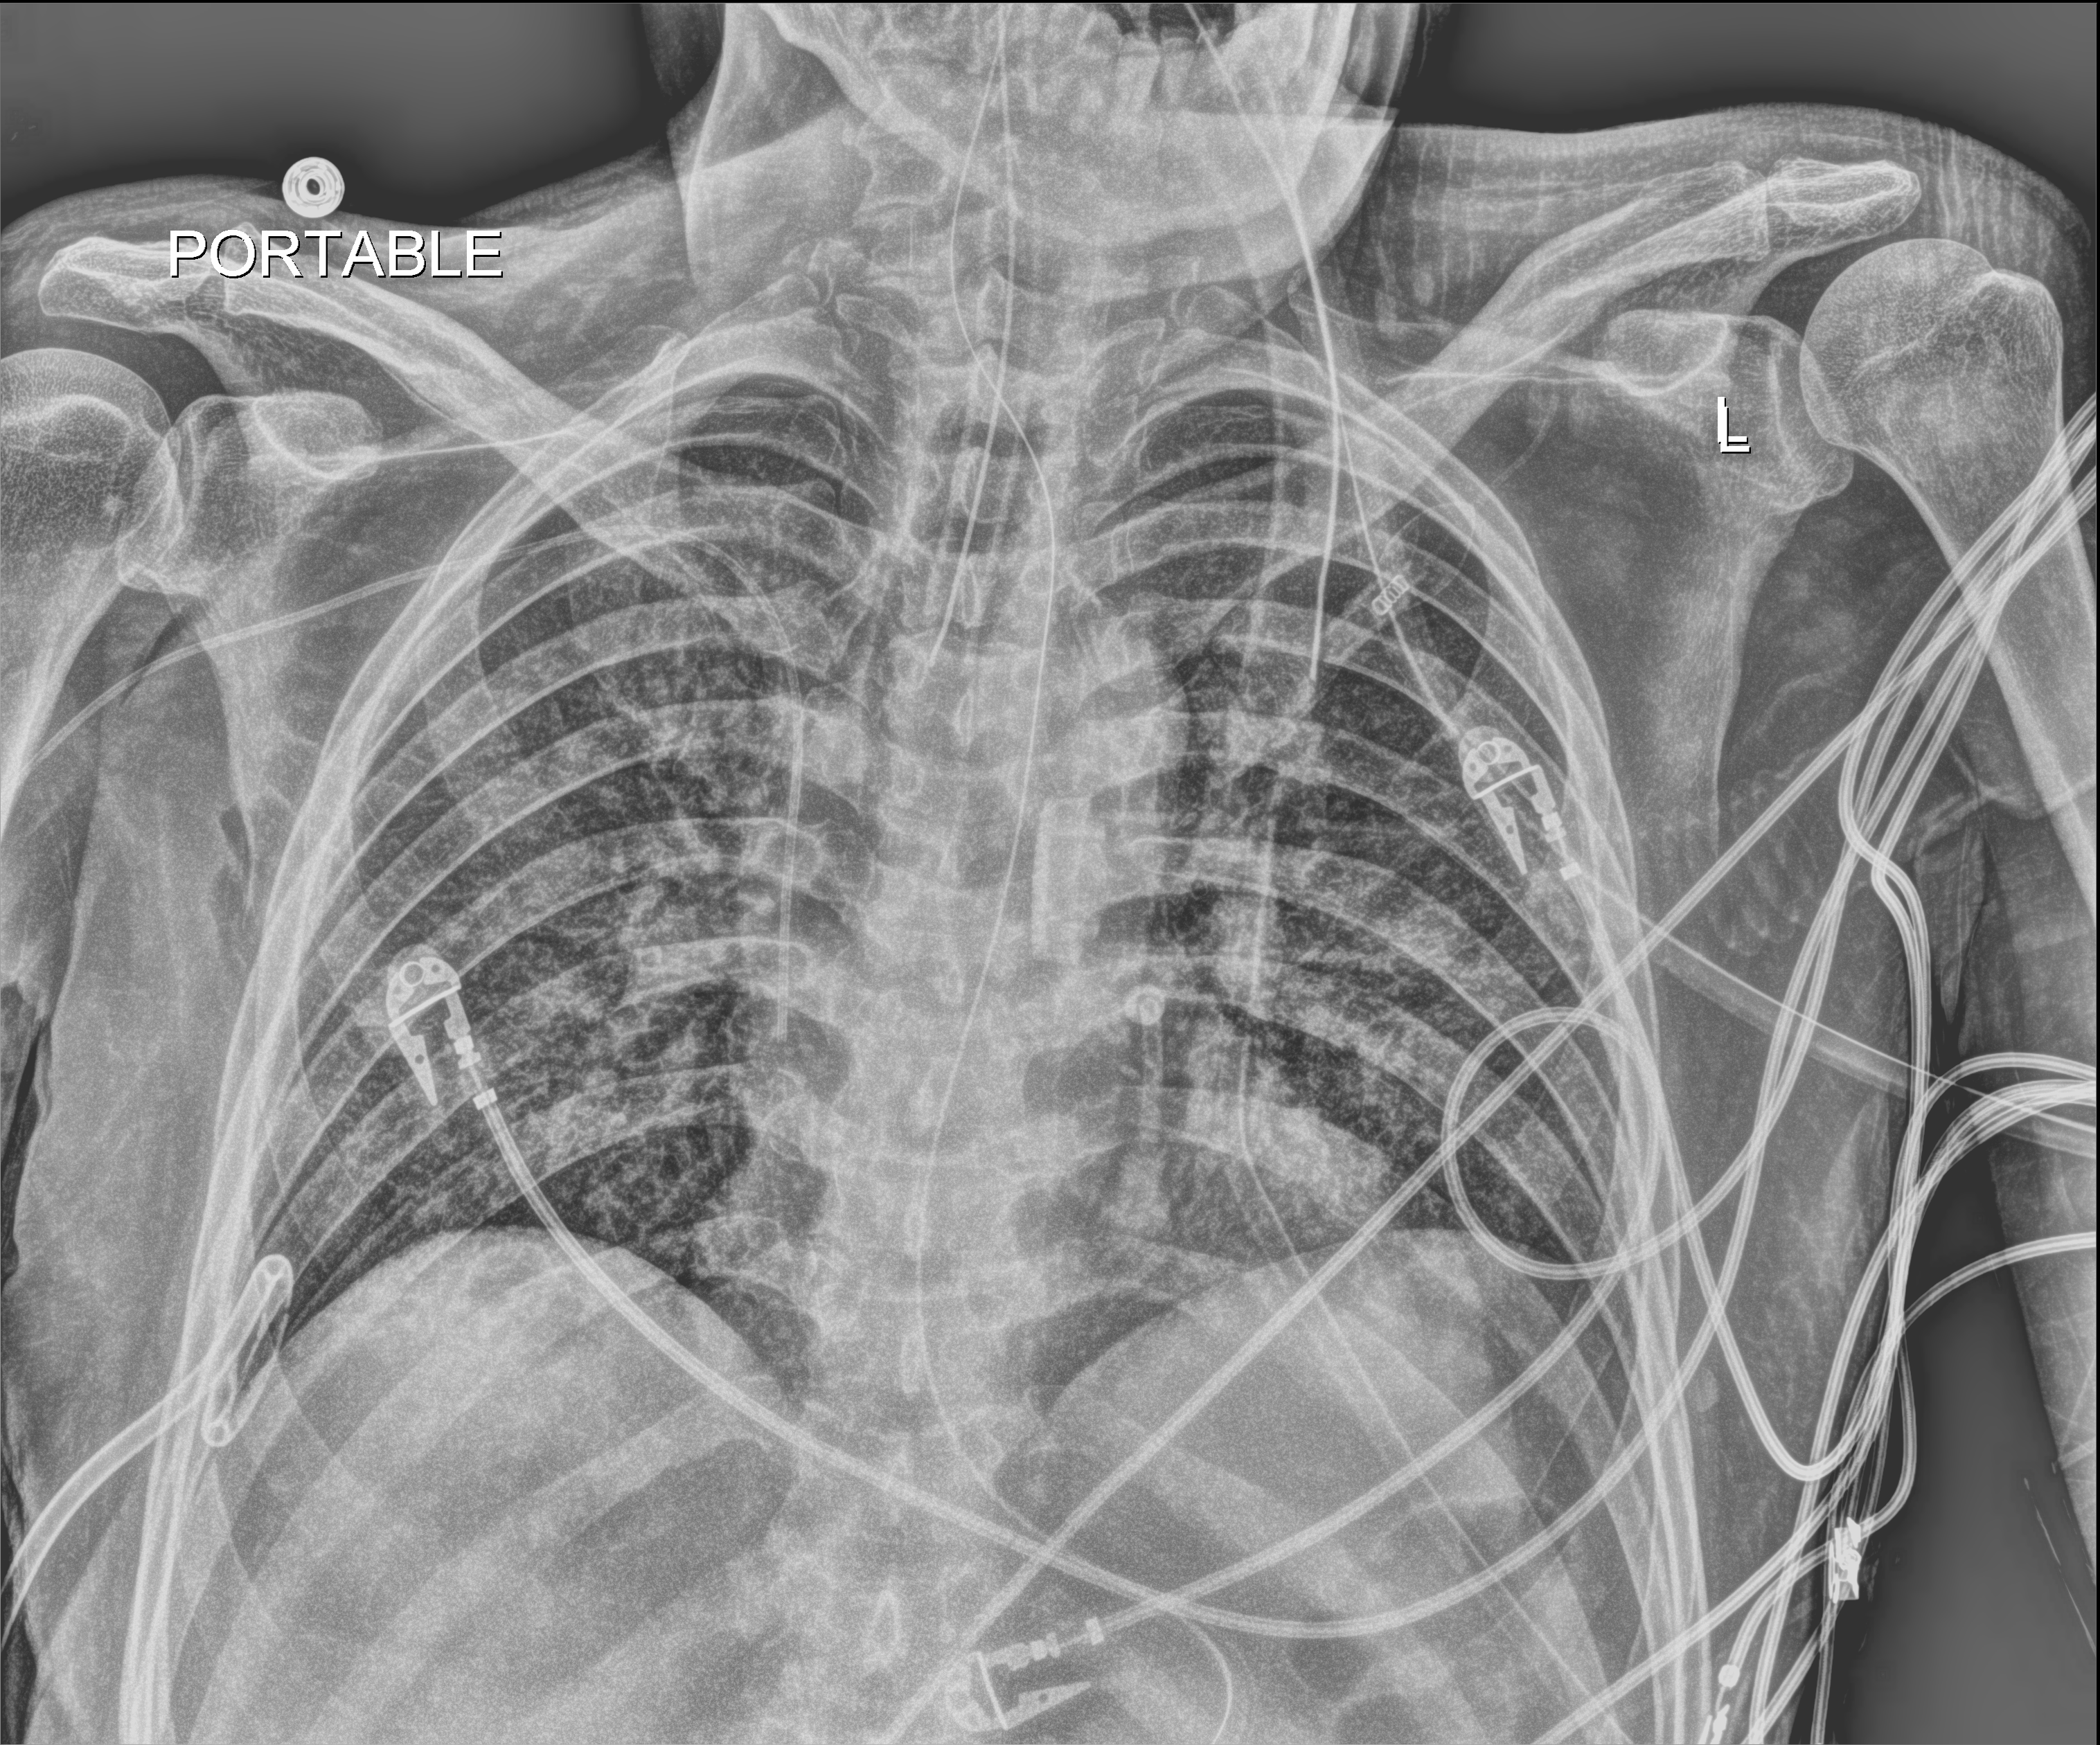
Chest X-ray (portable), anteroposterior (AP) projection. Patient hospitalised with COVID-19; male, aged 18–59 years.
Hospital-stay facts (about this admission, not read from this image; timing relative to this image not recorded):
- diabetes (admission record): no